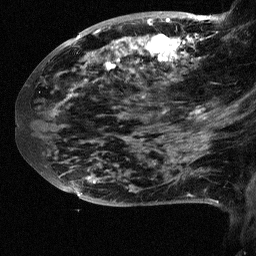
Breast MRI (dynamic contrast-enhanced), one sagittal slice. Position 27 of 64 along the scan axis. Dynamic contrast-enhanced study with each time point stored as its own series, time point 2 of 3 at this slice position (early post-contrast, ordered by acquisition time). 1.5 T. TE 4.5 ms, TR 11 ms. 2.5 mm slice thickness. 256 × 256 image matrix. Female patient, age 38 years. Case-level facts recorded for this patient, not image findings: setting: breast cancer imaged before/during neoadjuvant chemotherapy; receptor status: HR-positive, HER2-negative.
Structures marked on this image (semi-automatic segmentation, software-assisted and operator-edited):
- analysis volume of interest (the breast-tissue region the enhancement analysis was run in; not a lesion): box from (x=88, y=18) to (x=252, y=126) px
- tumour enhancement mask (voxels above the 90 % enhancement threshold inside the analysis volume of interest): (x=106, y=18)–(x=218, y=113)